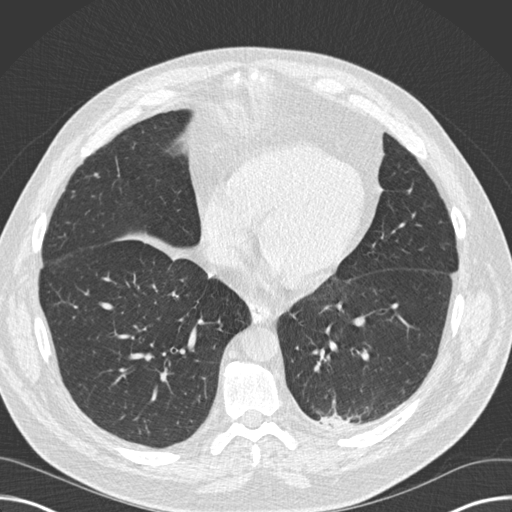
Low-dose screening chest CT, one axial slice. Position 56 of 160 along the scan axis. Reconstruction kernel B30f. 120 kVp. Lung window (W 1500 / L -600 HU). 2 mm slice thickness. 512 × 512 image matrix.
Annotated regions visible in this slice (expert manual segmentation):
- lesion 1 (tumor, upper lobe of left lung): bounding box <321,413,350,427> (left, top, right, bottom; pixels)